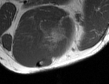
MRI of an extremity soft-tissue mass, one axial slice. Slice 40 of 50 in the series (ordered by position). MR volume resampled by the dataset authors to the PET/CT grid (not the native acquisition matrix). 109 × 84 image matrix. Male patient. Case-level facts recorded for this patient, not image findings: histological type: synovial sarcoma; site of the primary tumour: left poplietal fossa.
Outlined on this slice (expert contour drawn on MRI and transferred to this co-registered scan by the dataset authors):
- gross tumour volume (mass): bounding box (x1, y1, x2, y2) in pixels: (39, 28, 61, 52)